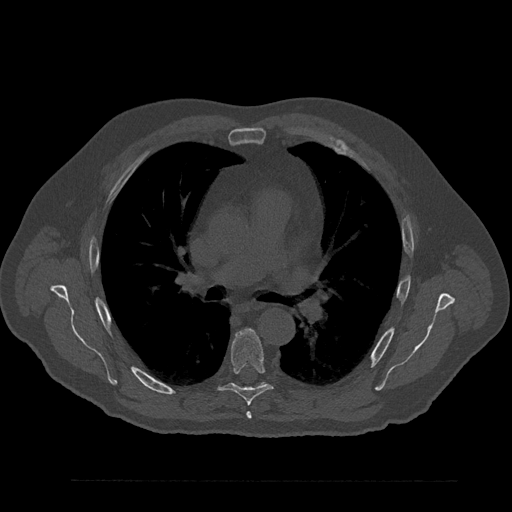
CT including the spine, one axial slice; slice 555 of 797 in the series (ordered by position); reconstruction kernel Br40s/3; 120 kVp; bone window (W 1800 / L 400 HU); 512 × 512 image matrix, field of view 430 × 430 mm. Male patient, age 61 years. Case-level facts recorded for this patient, not image findings: primary cancer: prostate.
Outlined on this slice (semi-automatic segmentation, software-assisted and operator-edited):
- T5 vertebra: bounding box [x1, y1, x2, y2] px = [246, 412, 252, 419]
- T6 vertebra: [212, 329, 273, 406]
- T7 vertebra: [261, 383, 265, 384]